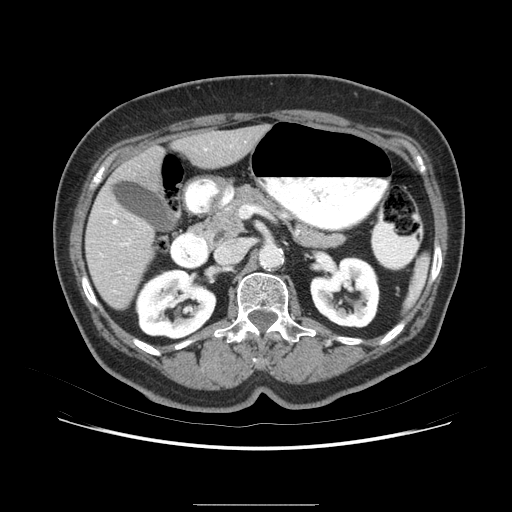
Contrast-enhanced abdominal CT (liver protocol), one axial slice. Position 33 of 79 along the scan axis. 120 kVp. Soft-tissue window (W 400 / L 40 HU). 2.5 mm slice thickness. 512 × 512 image matrix. Case-level facts recorded for this patient, not image findings: diagnosis: hepatocellular carcinoma (patient treated with transarterial chemoembolisation; whether this scan precedes or follows treatment is not stated here); TNM stage (as recorded): Stage-I; Child-Pugh class: A; tumour differentiation: poorly differentiated; tumour nodularity: uninodular.
Outlined on this slice (semi-automatically segmented with operator editing):
- liver parenchyma outside the tumour (the mass and vessels are separate outlines, so this box may not span the whole liver): bounding box (x1, y1, x2, y2) in pixels: (84, 122, 276, 322)
- mass: (95, 198, 152, 232)
- liver vessels: (111, 151, 238, 286)